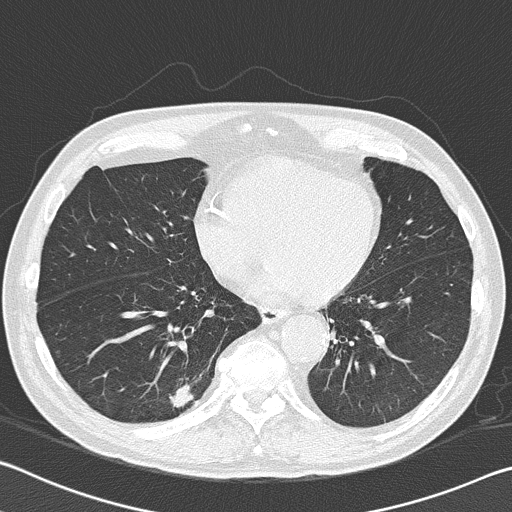
Low-dose screening chest CT, axial slice. Baseline screening round. Lung window (W 1500 / L -600 HU). 120 kVp. Slice 113 of 168 in the series. Male participant, aged 74 years at enrolment. Current smoker at enrolment.
Expert reader's lesion annotation, bounding box (x1, y1, x2, y2) in pixels: (148, 368, 214, 428). Reader record for this screening exam (exam-level; its link to the box is not recorded): non-calcified nodule or mass ≥4 mm, right lower lobe, 13 × 11 mm, spiculated (stellate) margins, soft tissue attenuation. Official screen result: positive, change unspecified: nodule(s) >= 4 mm or enlarging nodule(s), mass(es), or other non-specific abnormalities suspicious for lung cancer. Lung cancer was diagnosed 414 days after this screen: bronchiolo-alveolar adenocarcinoma, NOS, right lower lobe, moderately differentiated (G2), stage IA (AJCC 6th edition), 16 mm at pathology.